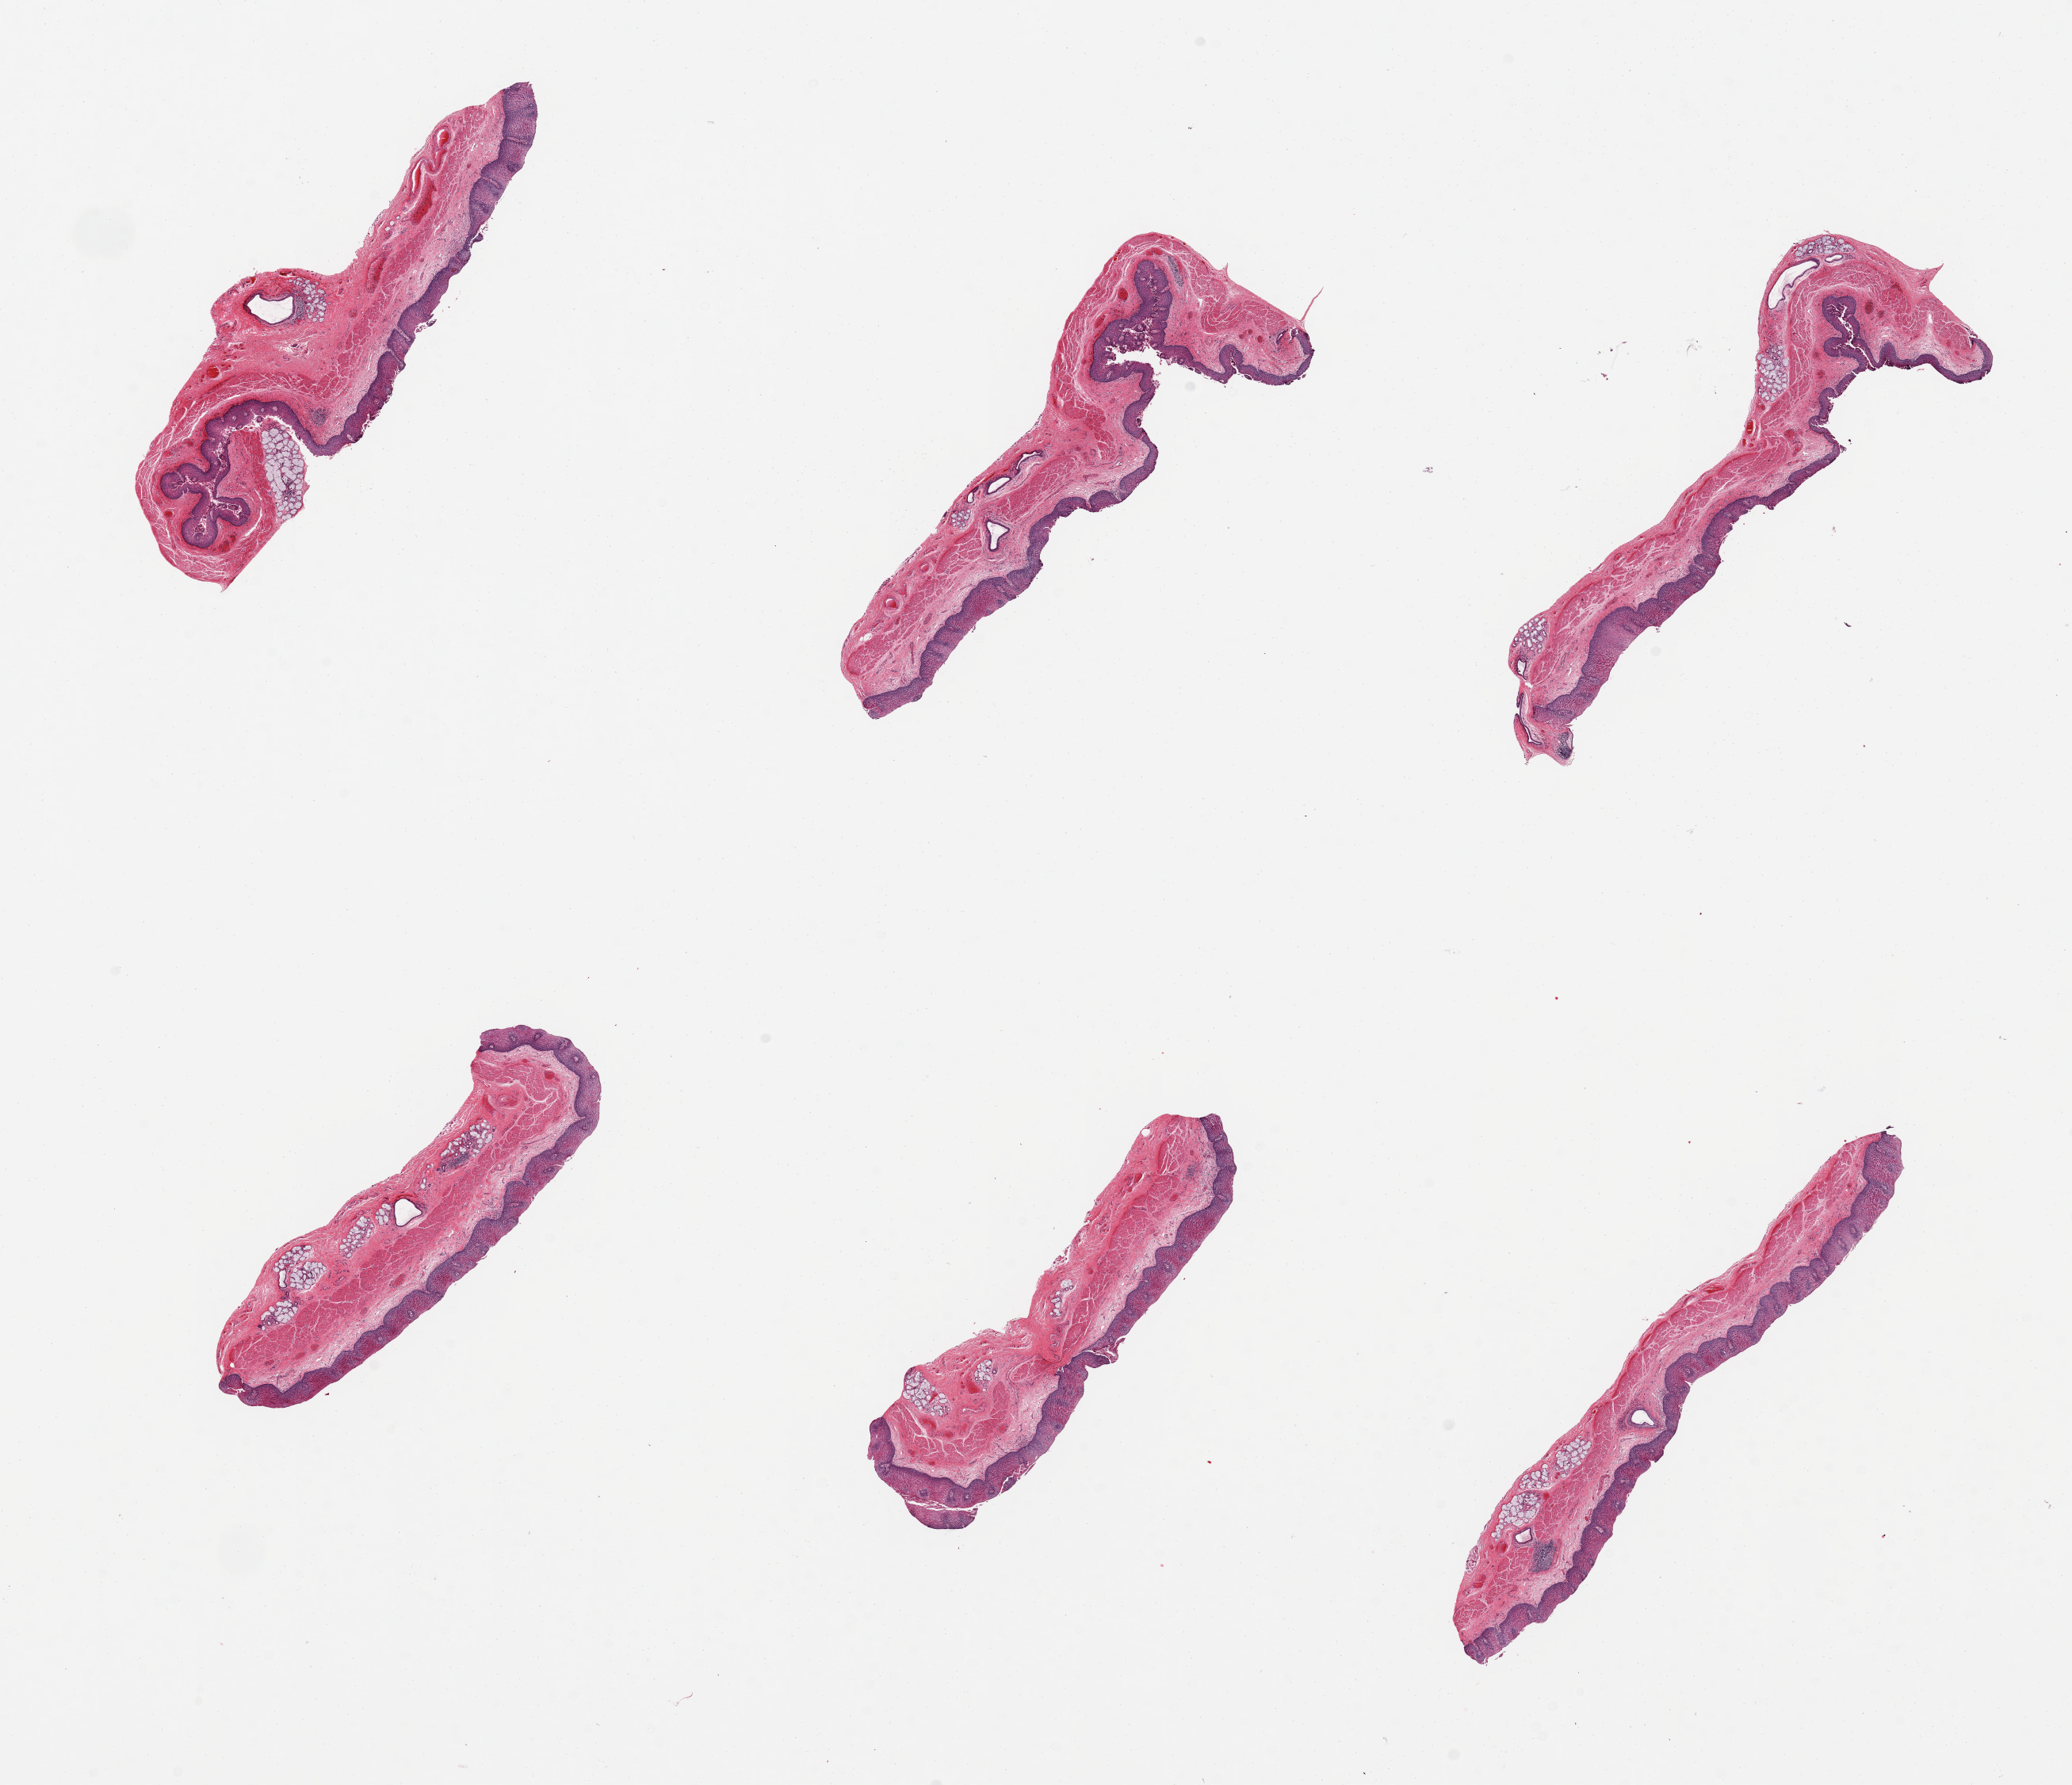
Digitized hematoxylin and eosin (H&E)-stained section, brightfield — a low-resolution overview of the entire scanned area, about 20.7 x 17.8 mm (slide scanned at 20x), PAXgene-fixed, paraffin-embedded tissue, sampled site (target tissue): esophageal mucous membrane, tissue donor sample. Donor: male.
Pathologist's review note for this sample: 6 pieces, several clusters of submucosal glands, few collections of lymphocytes.